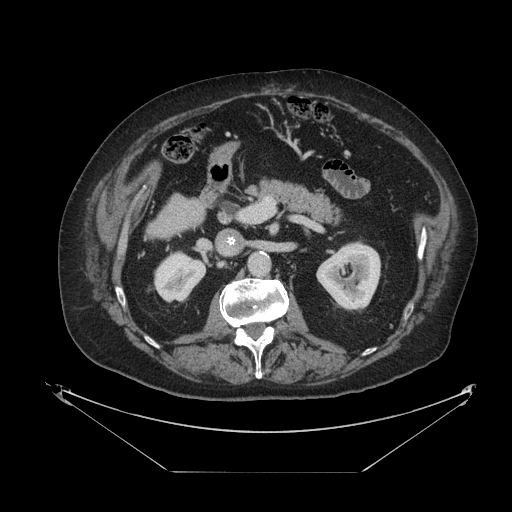
Contrast-enhanced abdominal CT, one axial slice. Position 39 of 121 along the scan axis. Reconstruction kernel STANDARD. 120 kVp. Intravenous contrast given. Soft-tissue window (W 400 / L 40 HU). 2.5 mm slice thickness. 512 × 512 image matrix. Male patient, age 68 years. From the clinical record (not read from this slice): diagnosis: colorectal cancer liver metastases, imaged before liver resection; multiple liver metastases: no.
Annotated regions visible in this slice (manually delineated by an expert):
- liver: bounding box (x1, y1, x2, y2) in pixels: (151, 197, 204, 235)
- planned liver remnant (the part of the liver to remain after resection): (151, 196, 204, 235)